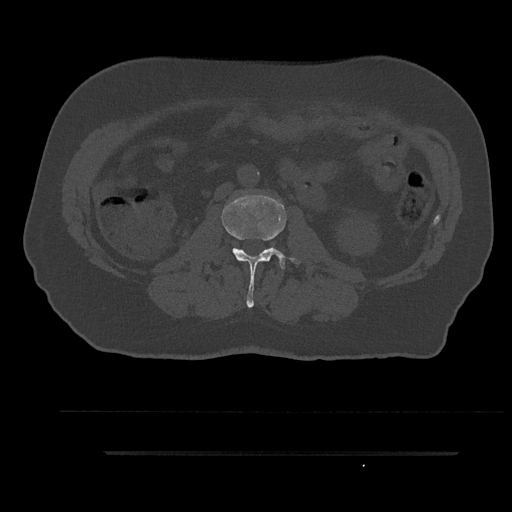
CT including the spine, one axial slice. Position 98 of 797 along the scan axis. Reconstruction kernel Br40s/3. Bone window (W 1800 / L 400 HU). 0.5 mm slice thickness. 512 × 512 image matrix, field of view 432 × 432 mm. Male patient, age 63 years. Case-level facts recorded for this patient, not image findings: primary cancer: renal; vertebrae with lytic lesions (as recorded): T8.
Outlined on this slice (semi-automatic segmentation, software-assisted and operator-edited):
- L2 vertebra: bounding box (x1, y1, x2, y2) in pixels: (222, 194, 300, 308)